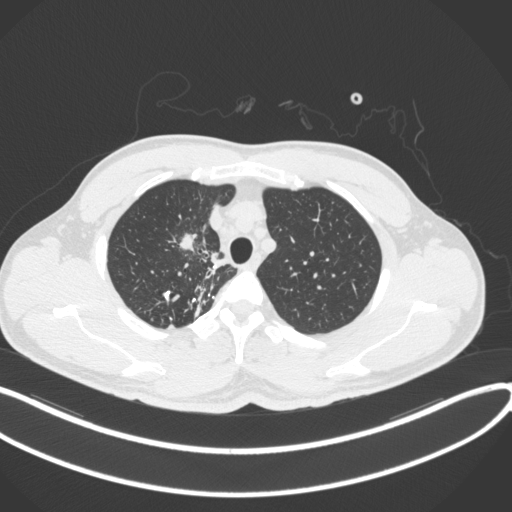
Chest CT, one axial slice. Position 304 of 391 along the scan axis. 120 kVp. Lung window (W 1500 / L -600 HU). 512 × 512 image matrix. Patient: male, 48 years. From the clinical record (not read from this slice): clinical TNM (as recorded): T1c N1 M1.
Outlined on this slice (bounding box drawn by a radiologist):
- lung tumour (recorded histology: adenocarcinoma): bounding box [x1, y1, x2, y2] px = [170, 225, 204, 256]